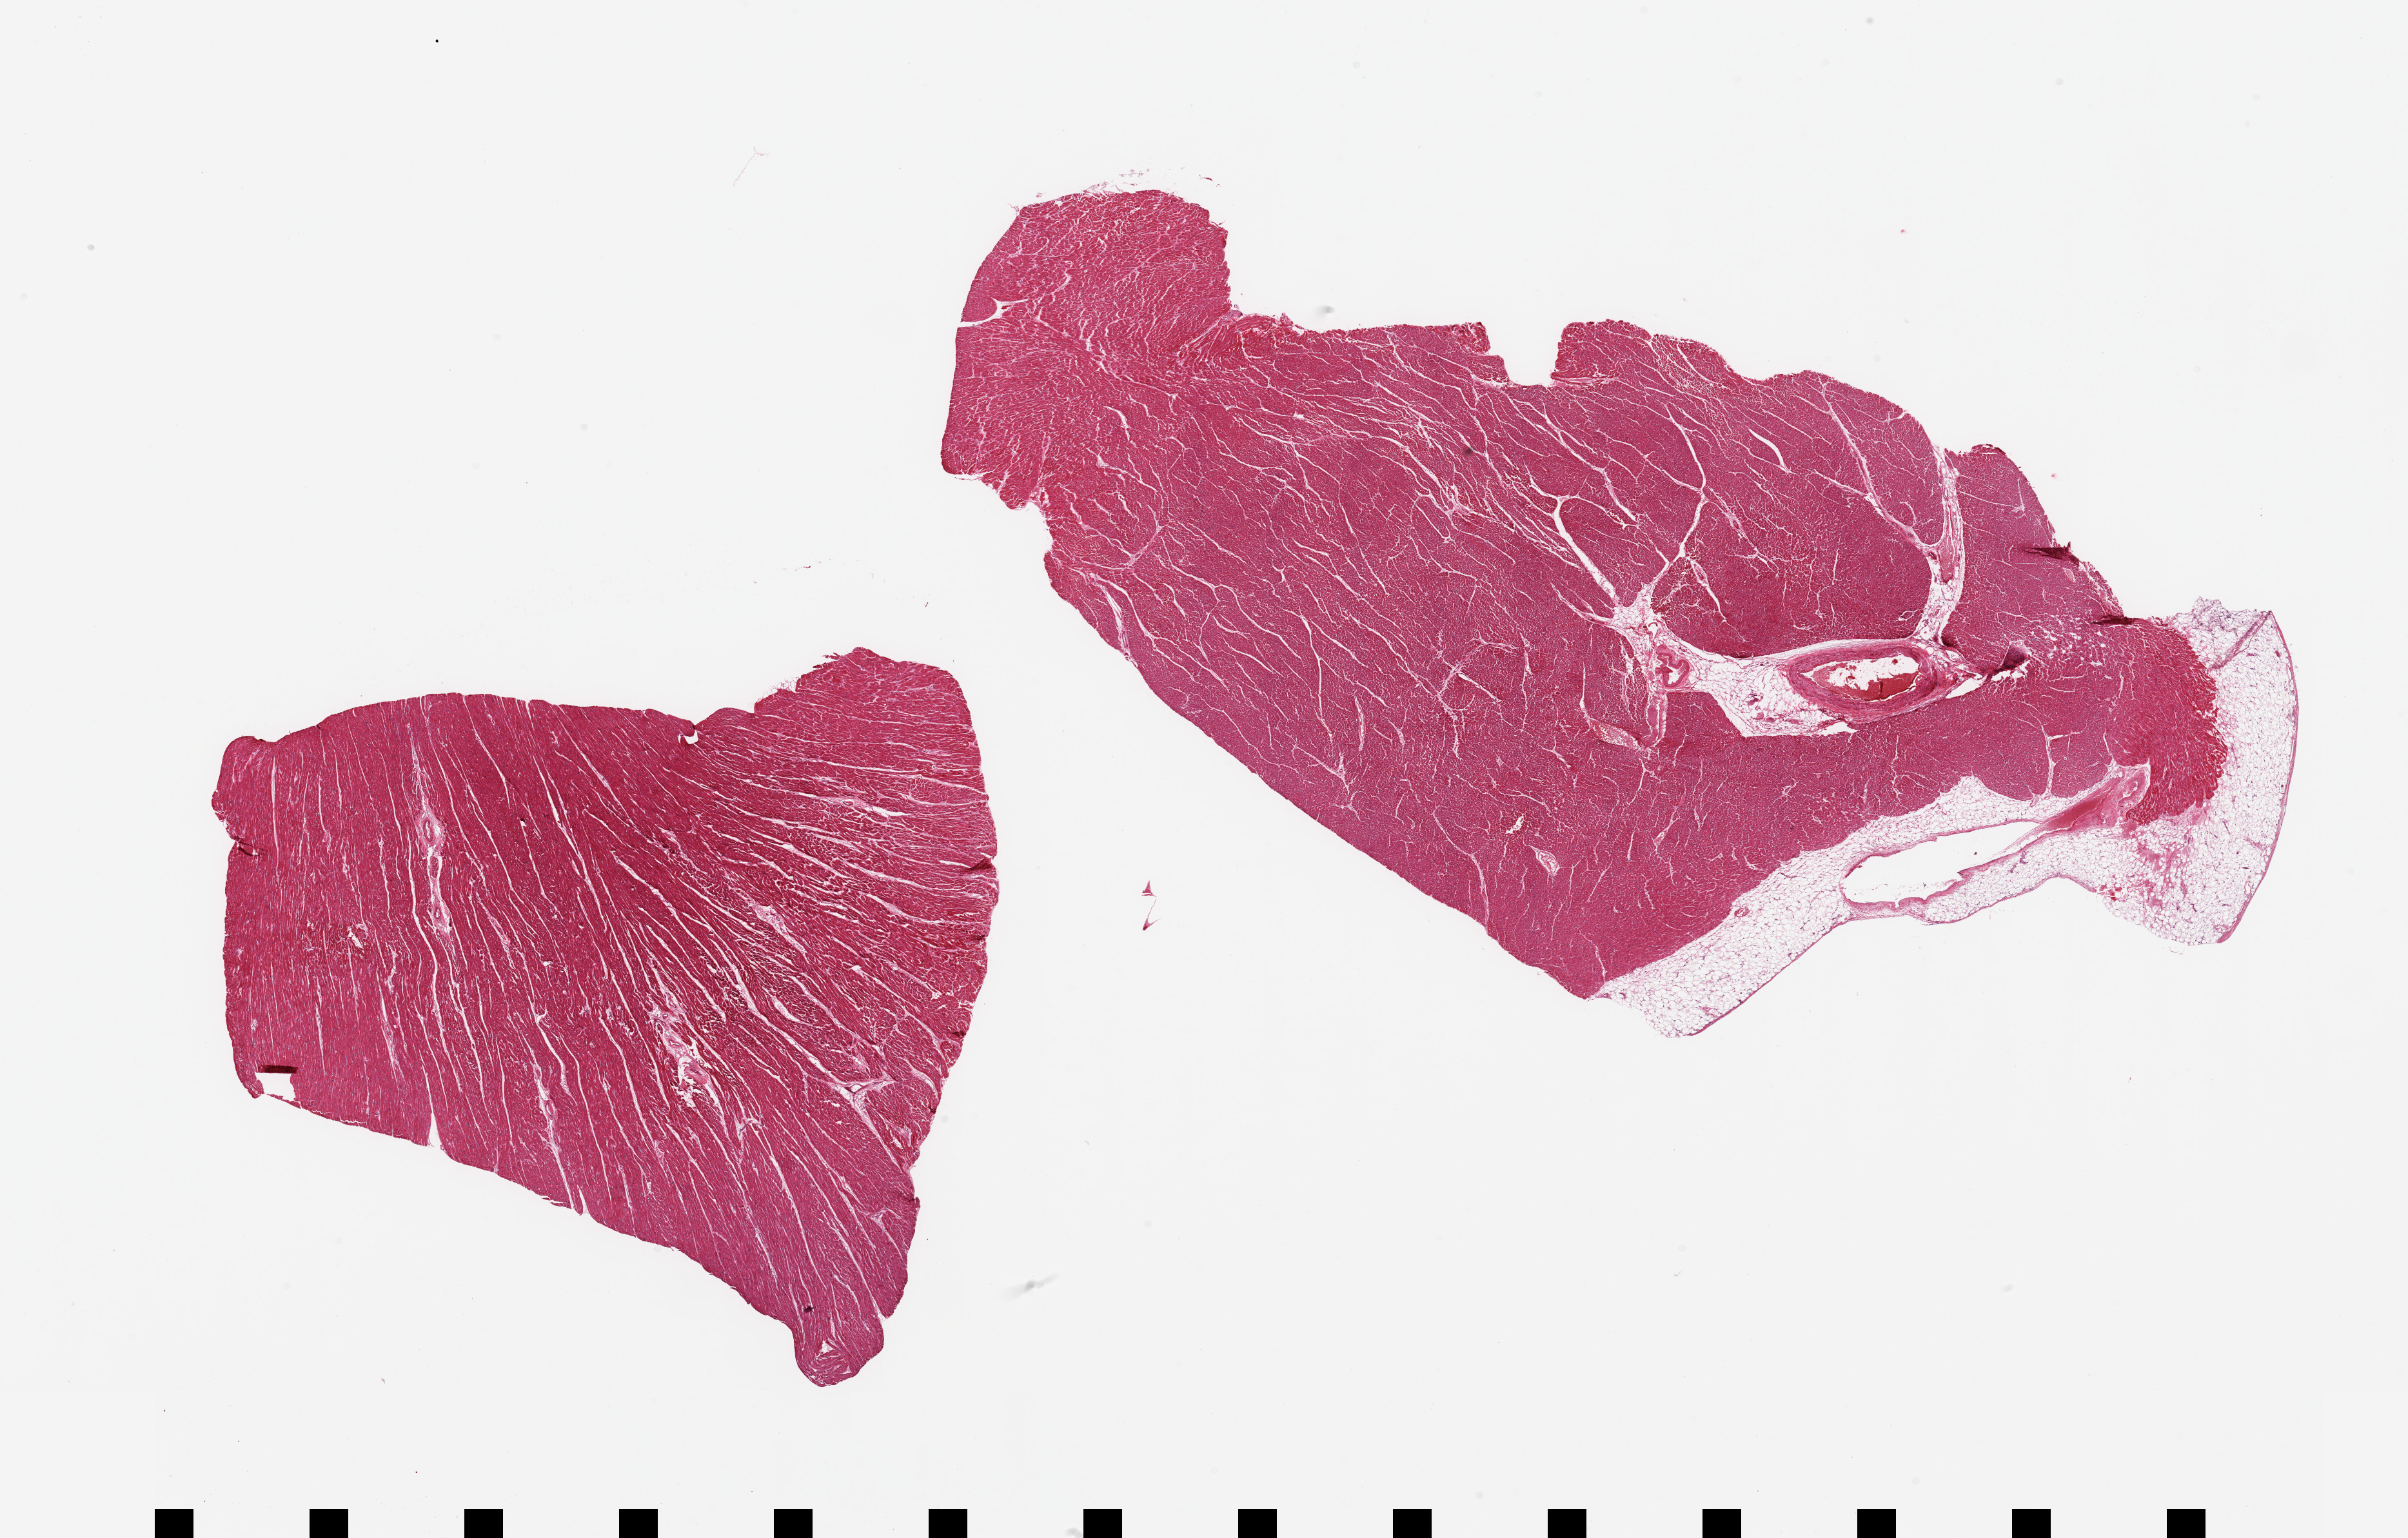
Haematoxylin and eosin whole-slide image — whole scanned area (about 29.5 x 18.9 mm, from a 20x scan) shown as a low-resolution overview; PAXgene-fixed, paraffin-embedded tissue; target tissue: heart; donor tissue sample. Female donor.
Pathologist's review note for this sample: 2 pieces; 1 piece has 0.8mm pericardial fat layer and a vein along 1 side, plus a 1 mm artery within the myocardium [all labeled].